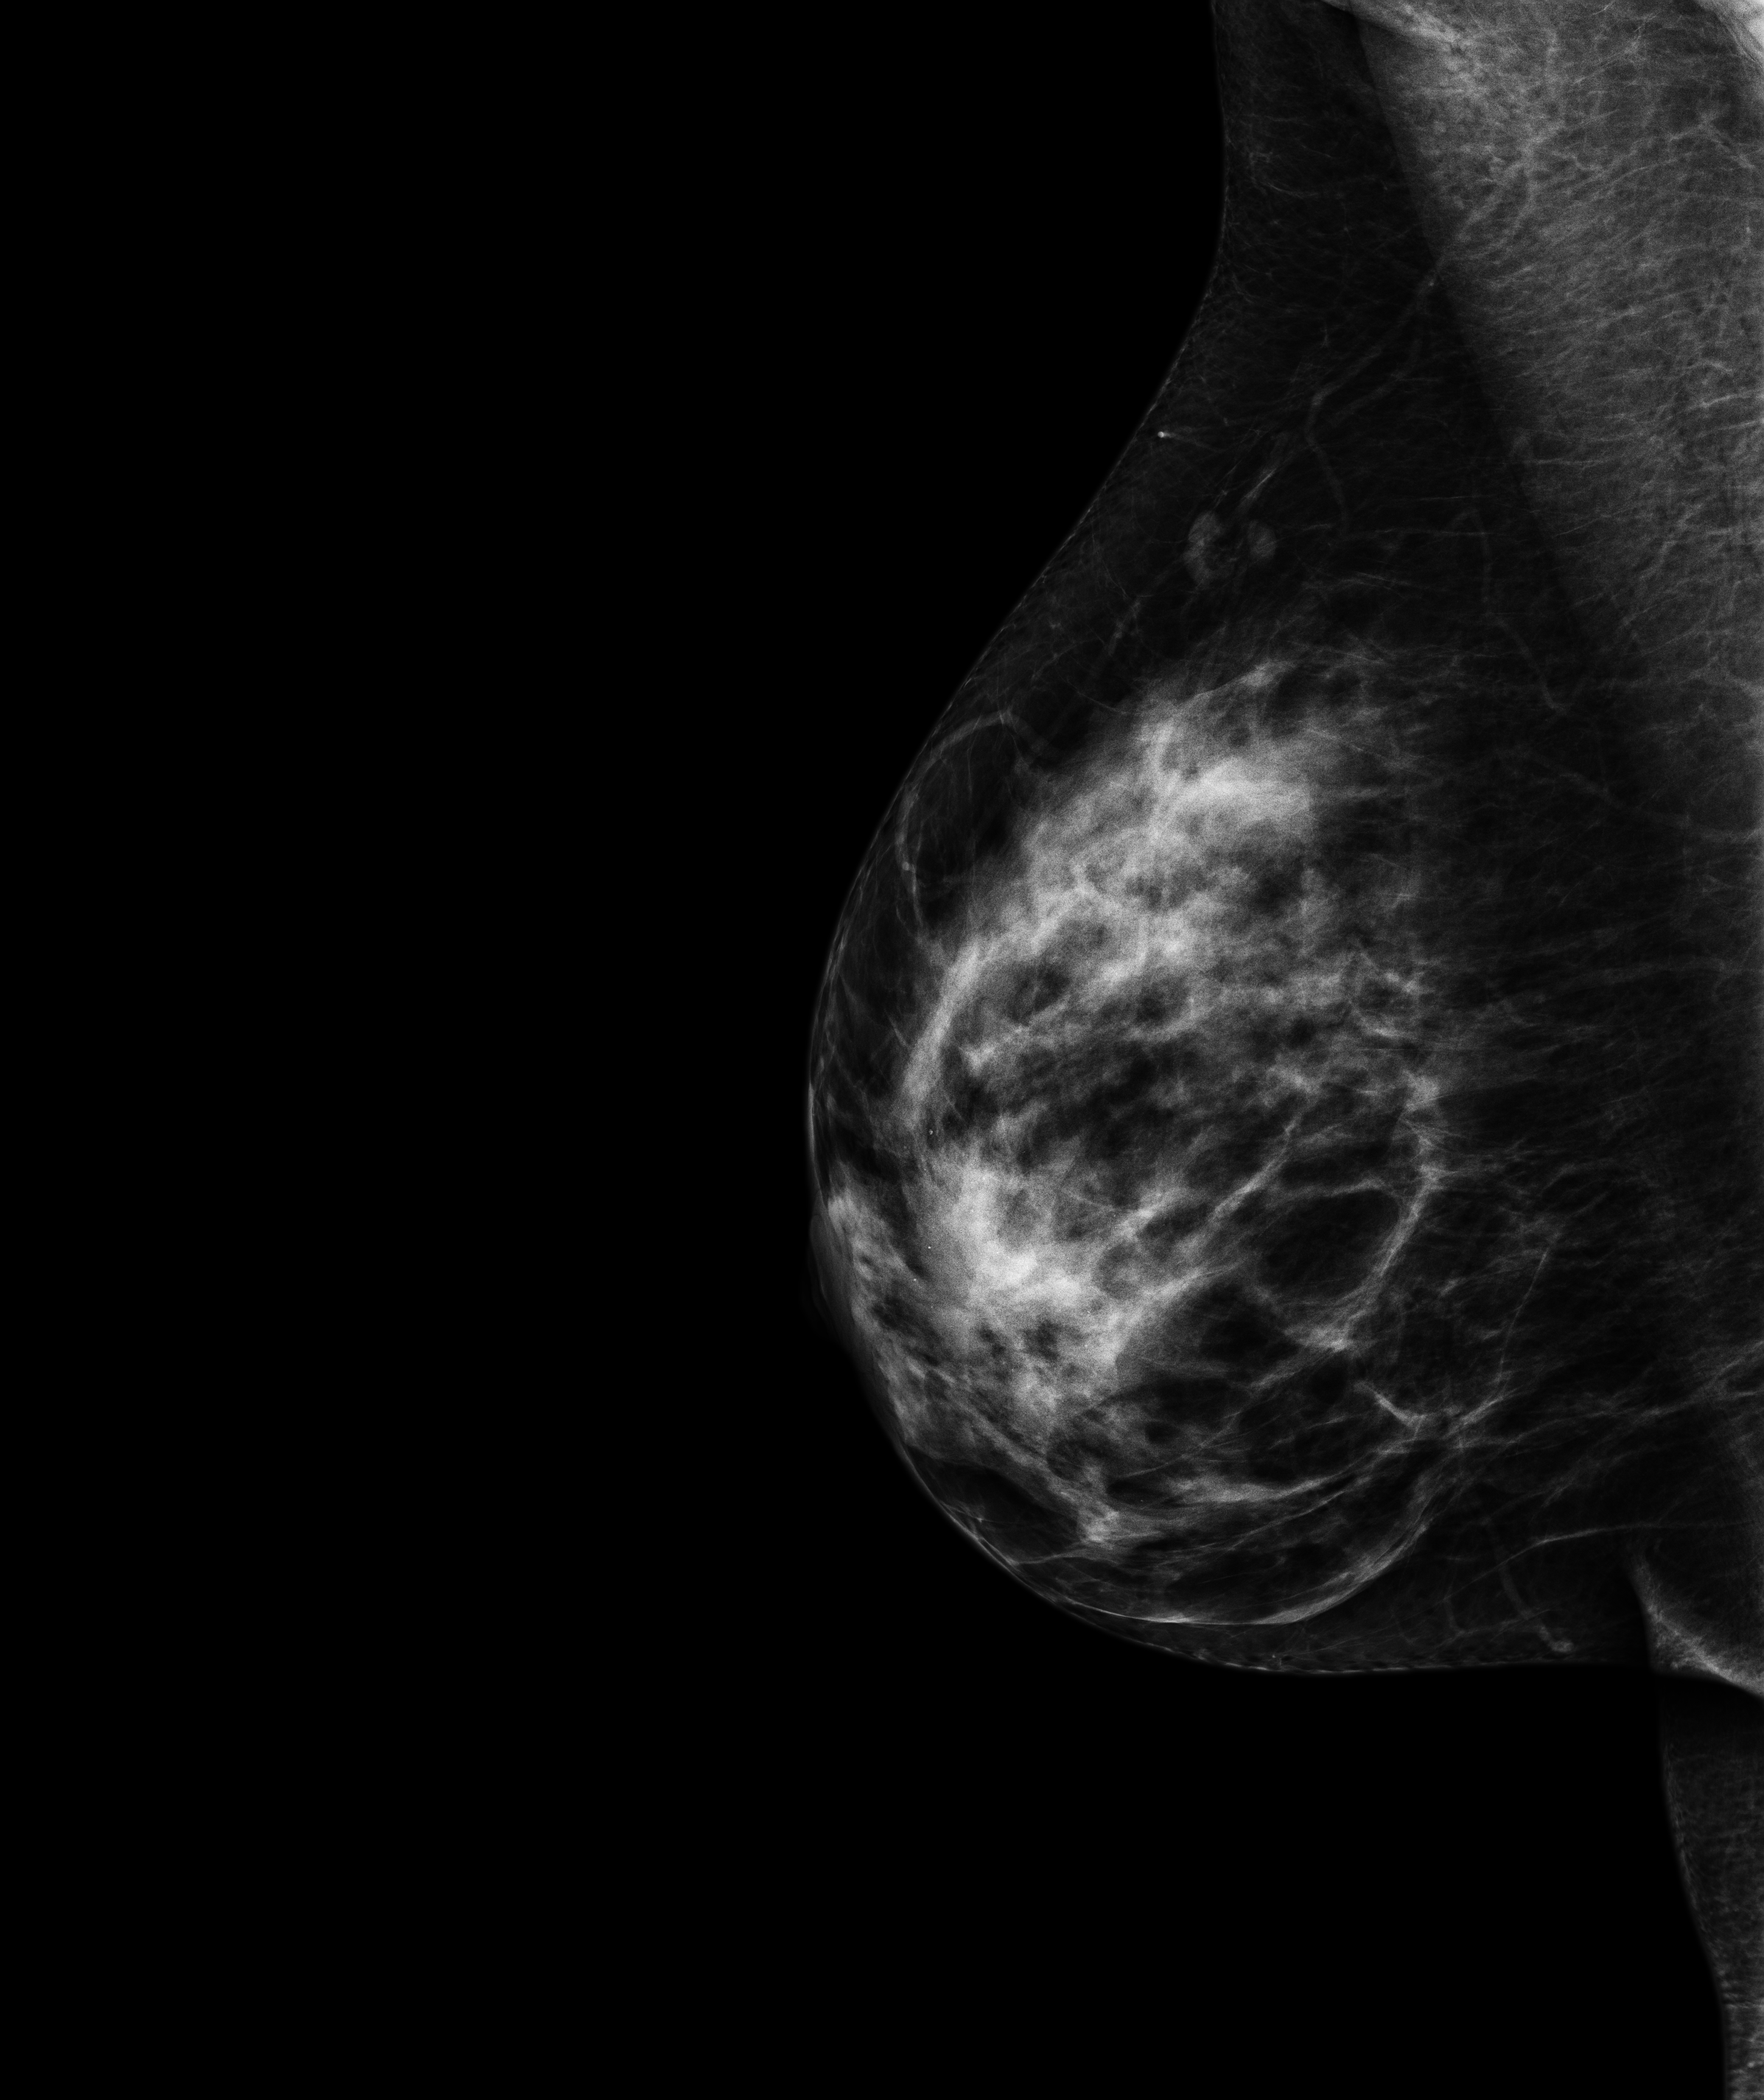
Annual screening mammography examination; compressed breast thickness 59.5 mm. Patient: female, 47 years.
Image type: full-field digital mammogram. Breast: right. Projection: MLO view.